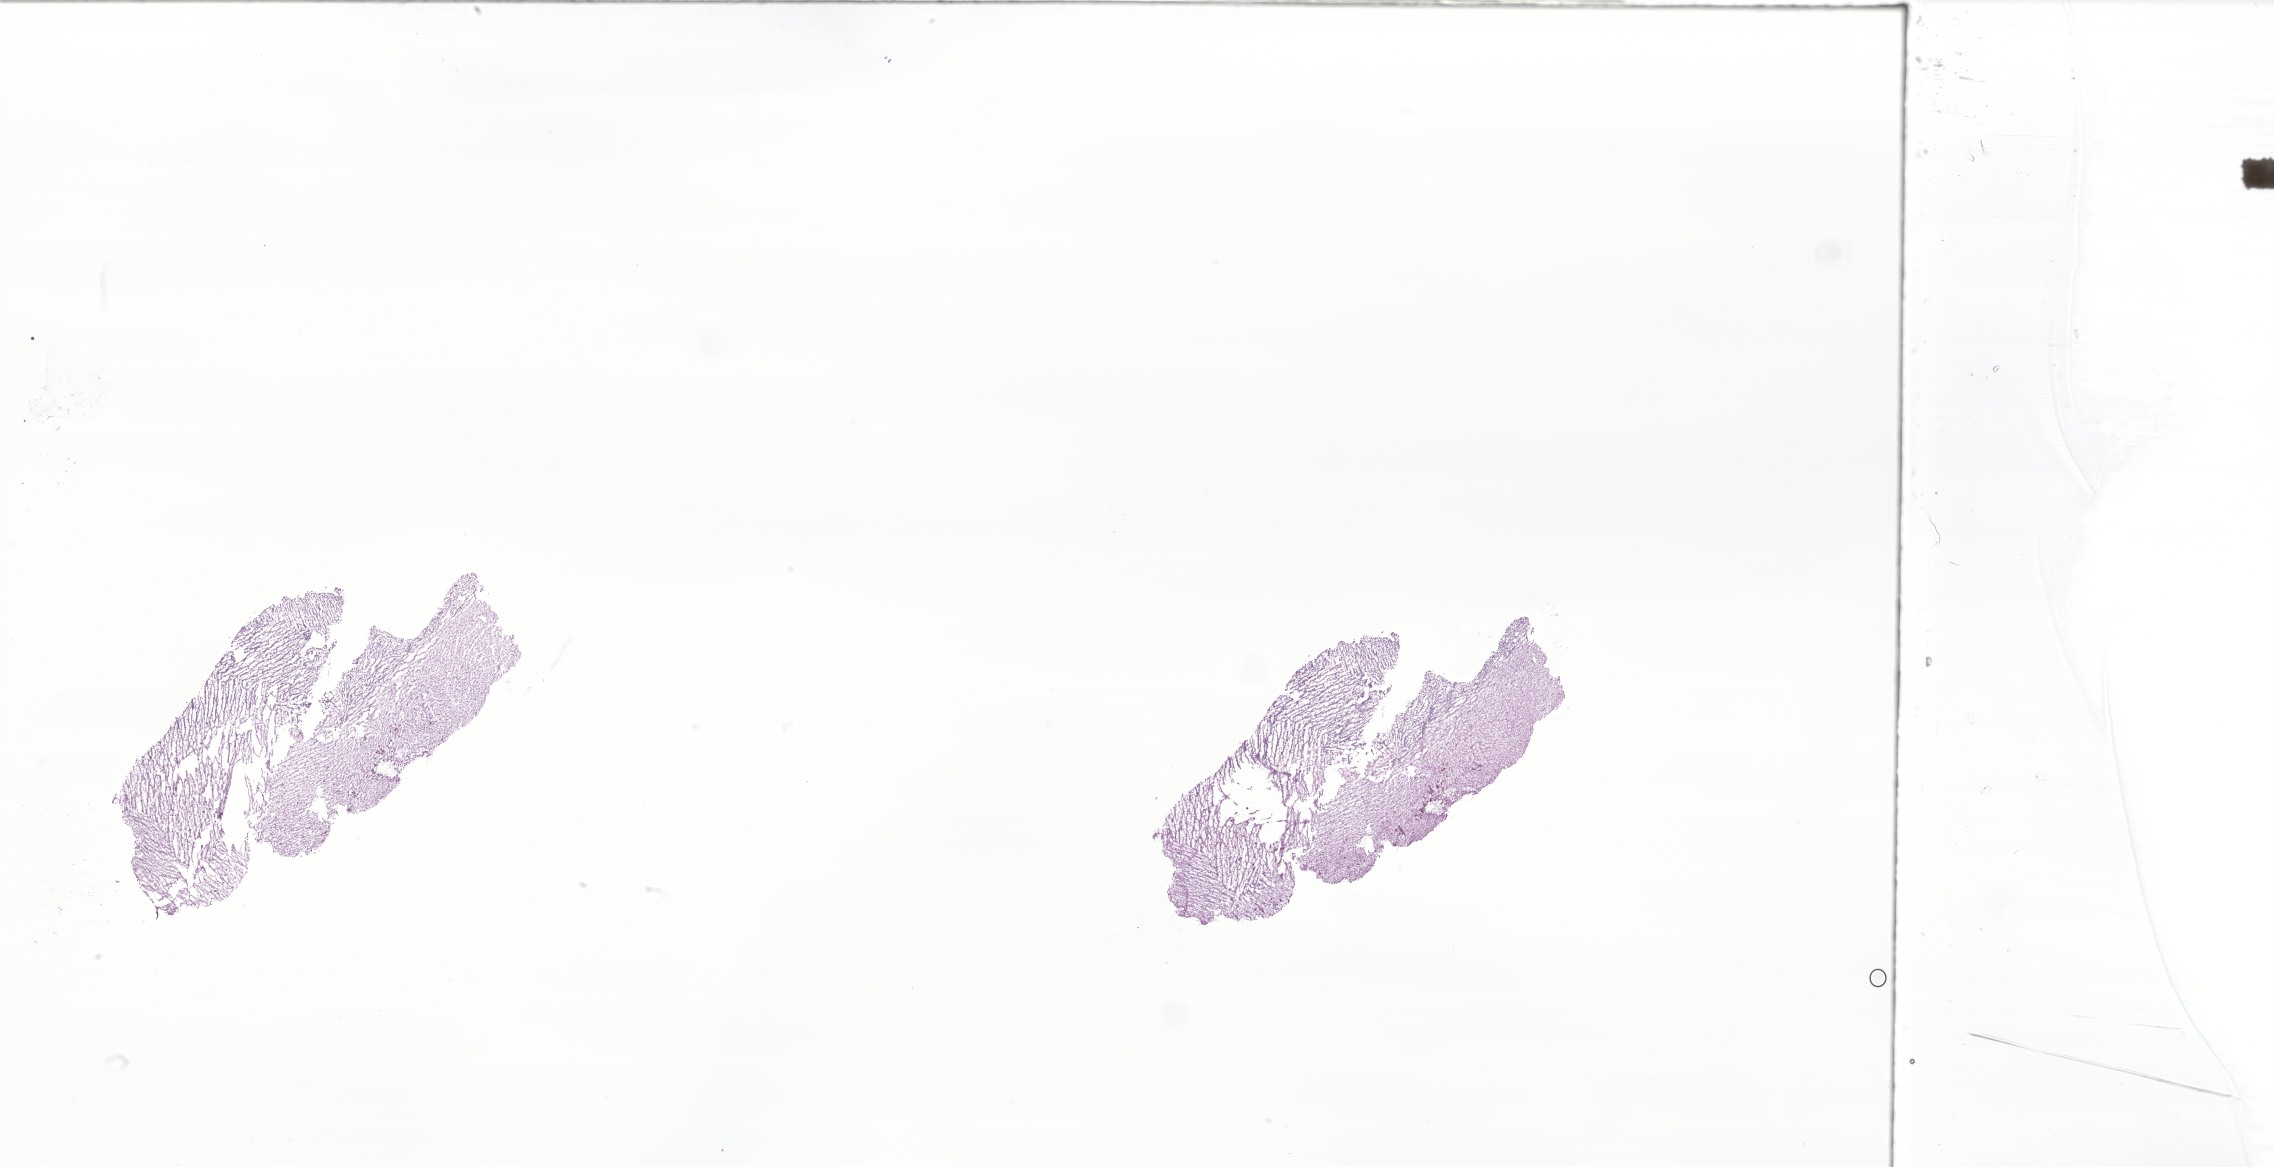
H&E whole-slide image of tumor tissue from the brain — shown as a low-resolution overview of the whole scanned area (about 38.4 x 19.7 mm), frozen section (OCT-embedded). Patient: female, age 77 months (6 years 5 months).
Diagnosis: Ependymoma, anaplastic.